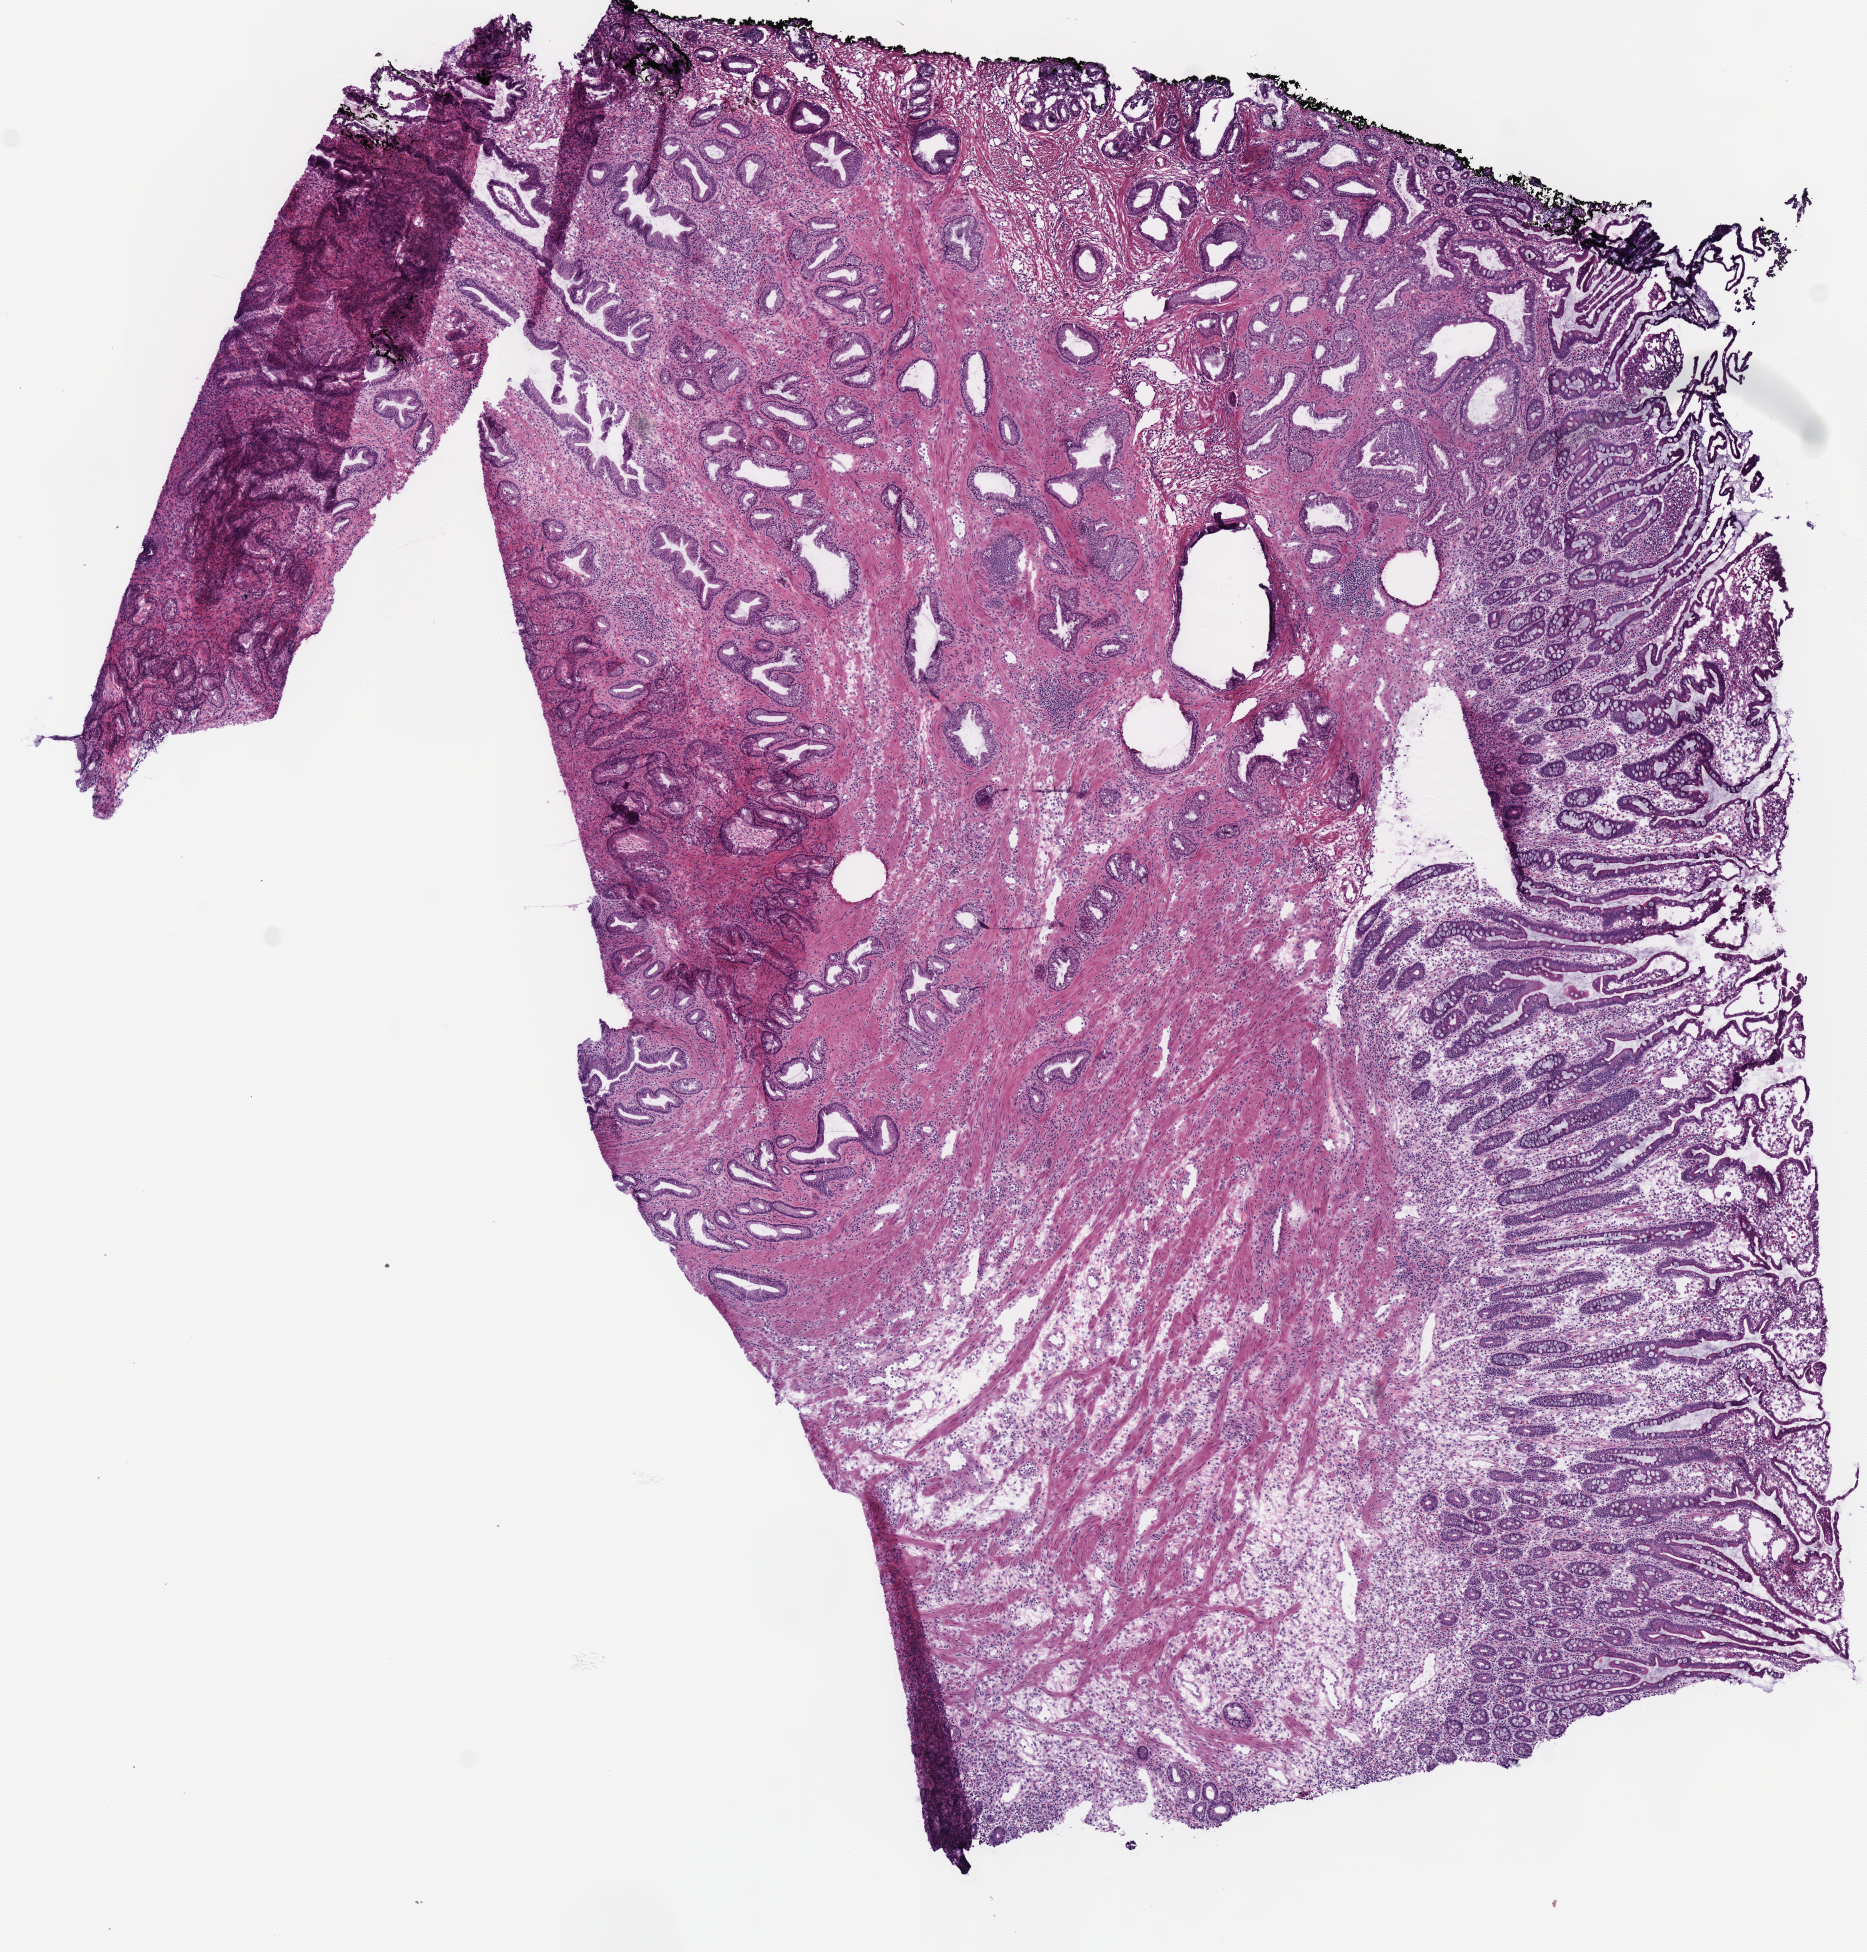
Digitized H&E-stained tissue section (whole slide) — shown as a low-resolution overview of the whole scanned area (about 7.3 x 7.7 mm, slide scanned at 40x); frozen section; sample: primary tumour, pancreas. Female patient; age at initial diagnosis 60 years. Histologic grade: G2 (moderately differentiated).
• diagnosis: Infiltrating duct carcinoma, NOS (head of pancreas)
• AJCC pathologic stage: IIA (7th edition)
• lymph nodes positive (case pathology): 0 of 17 examined